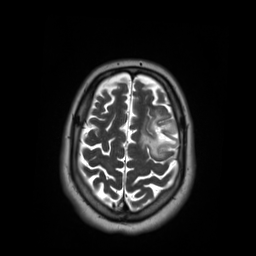
Brain MRI from a brain-tumour surgery series, one axial slice; slice 45 of 59 in the series (ordered by position); 3.03 mm slice thickness; 256 × 256 image matrix, field of view 250 × 250 mm. Case-level facts recorded for this patient, not image findings: histopathology: Oligodendroglioma; WHO grade: 2; IDH mutation: yes.
Annotated regions visible in this slice (outlined manually by an expert reader):
- tumour: box from (x=139, y=109) to (x=180, y=157) px